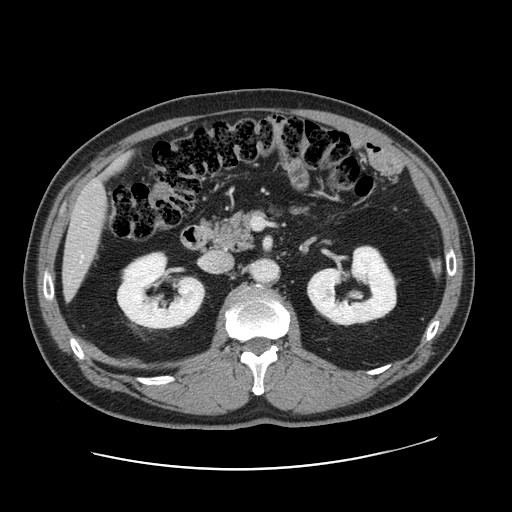
Contrast-enhanced abdominal CT, one axial slice; position 77 of 178 along the scan axis; 120 kVp; intravenous contrast given; soft-tissue window (W 400 / L 40 HU); 2.5 mm slice thickness; 512 × 512 image matrix, field of view 403 × 403 mm. Male patient, age 63 years. From the clinical record (not read from this slice): diagnosis: colorectal cancer liver metastases, imaged before liver resection; multiple liver metastases: yes; largest metastasis: 8 cm; disease in both lobes: yes.
Outlined on this slice (expert manual segmentation):
- liver: bounding box <63,178,107,295> (left, top, right, bottom; pixels)